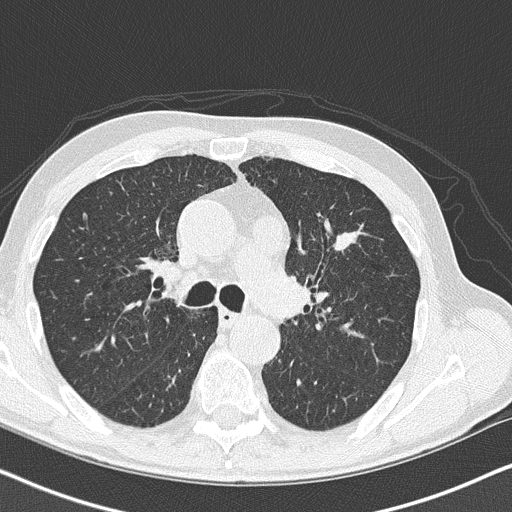
Low-dose screening chest CT, one axial slice. Slice 104 of 158 in the series (ordered by position). 120 kVp. Lung window (W 1500 / L -600 HU). 2 mm slice thickness. 512 × 512 image matrix, field of view 330 × 330 mm.
Structures marked on this image (manually delineated by an expert):
- lesion 1 (tumor, upper lobe of left lung): bounding box (x1, y1, x2, y2) in pixels: (336, 233, 354, 250)